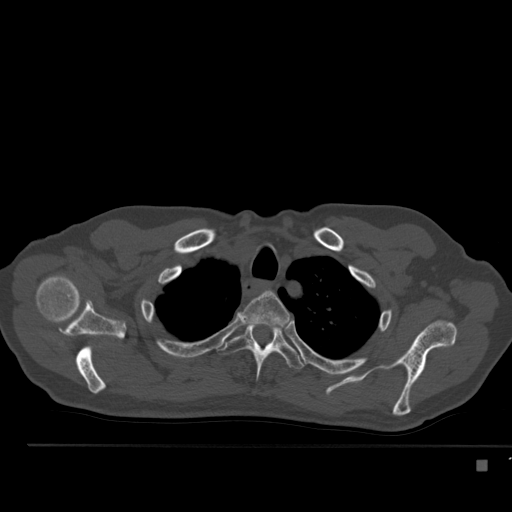
CT including the spine, one axial slice; slice 403 of 517 in the series (ordered by position); reconstruction kernel Br40s; 120 kVp; bone window (W 1800 / L 400 HU); 1.5 mm slice thickness; 512 × 512 image matrix, field of view 408 × 408 mm. Patient: male, 70 years. Case-level facts recorded for this patient, not image findings: primary cancer: renal; vertebrae with lytic lesions (as recorded): T4, T6, T10, T12, L3, L4, L5.
Structures marked on this image (semi-automatically segmented with operator editing):
- T2 vertebra: bounding box <241,291,290,328> (left, top, right, bottom; pixels)
- T3 vertebra: <217,323,305,381>